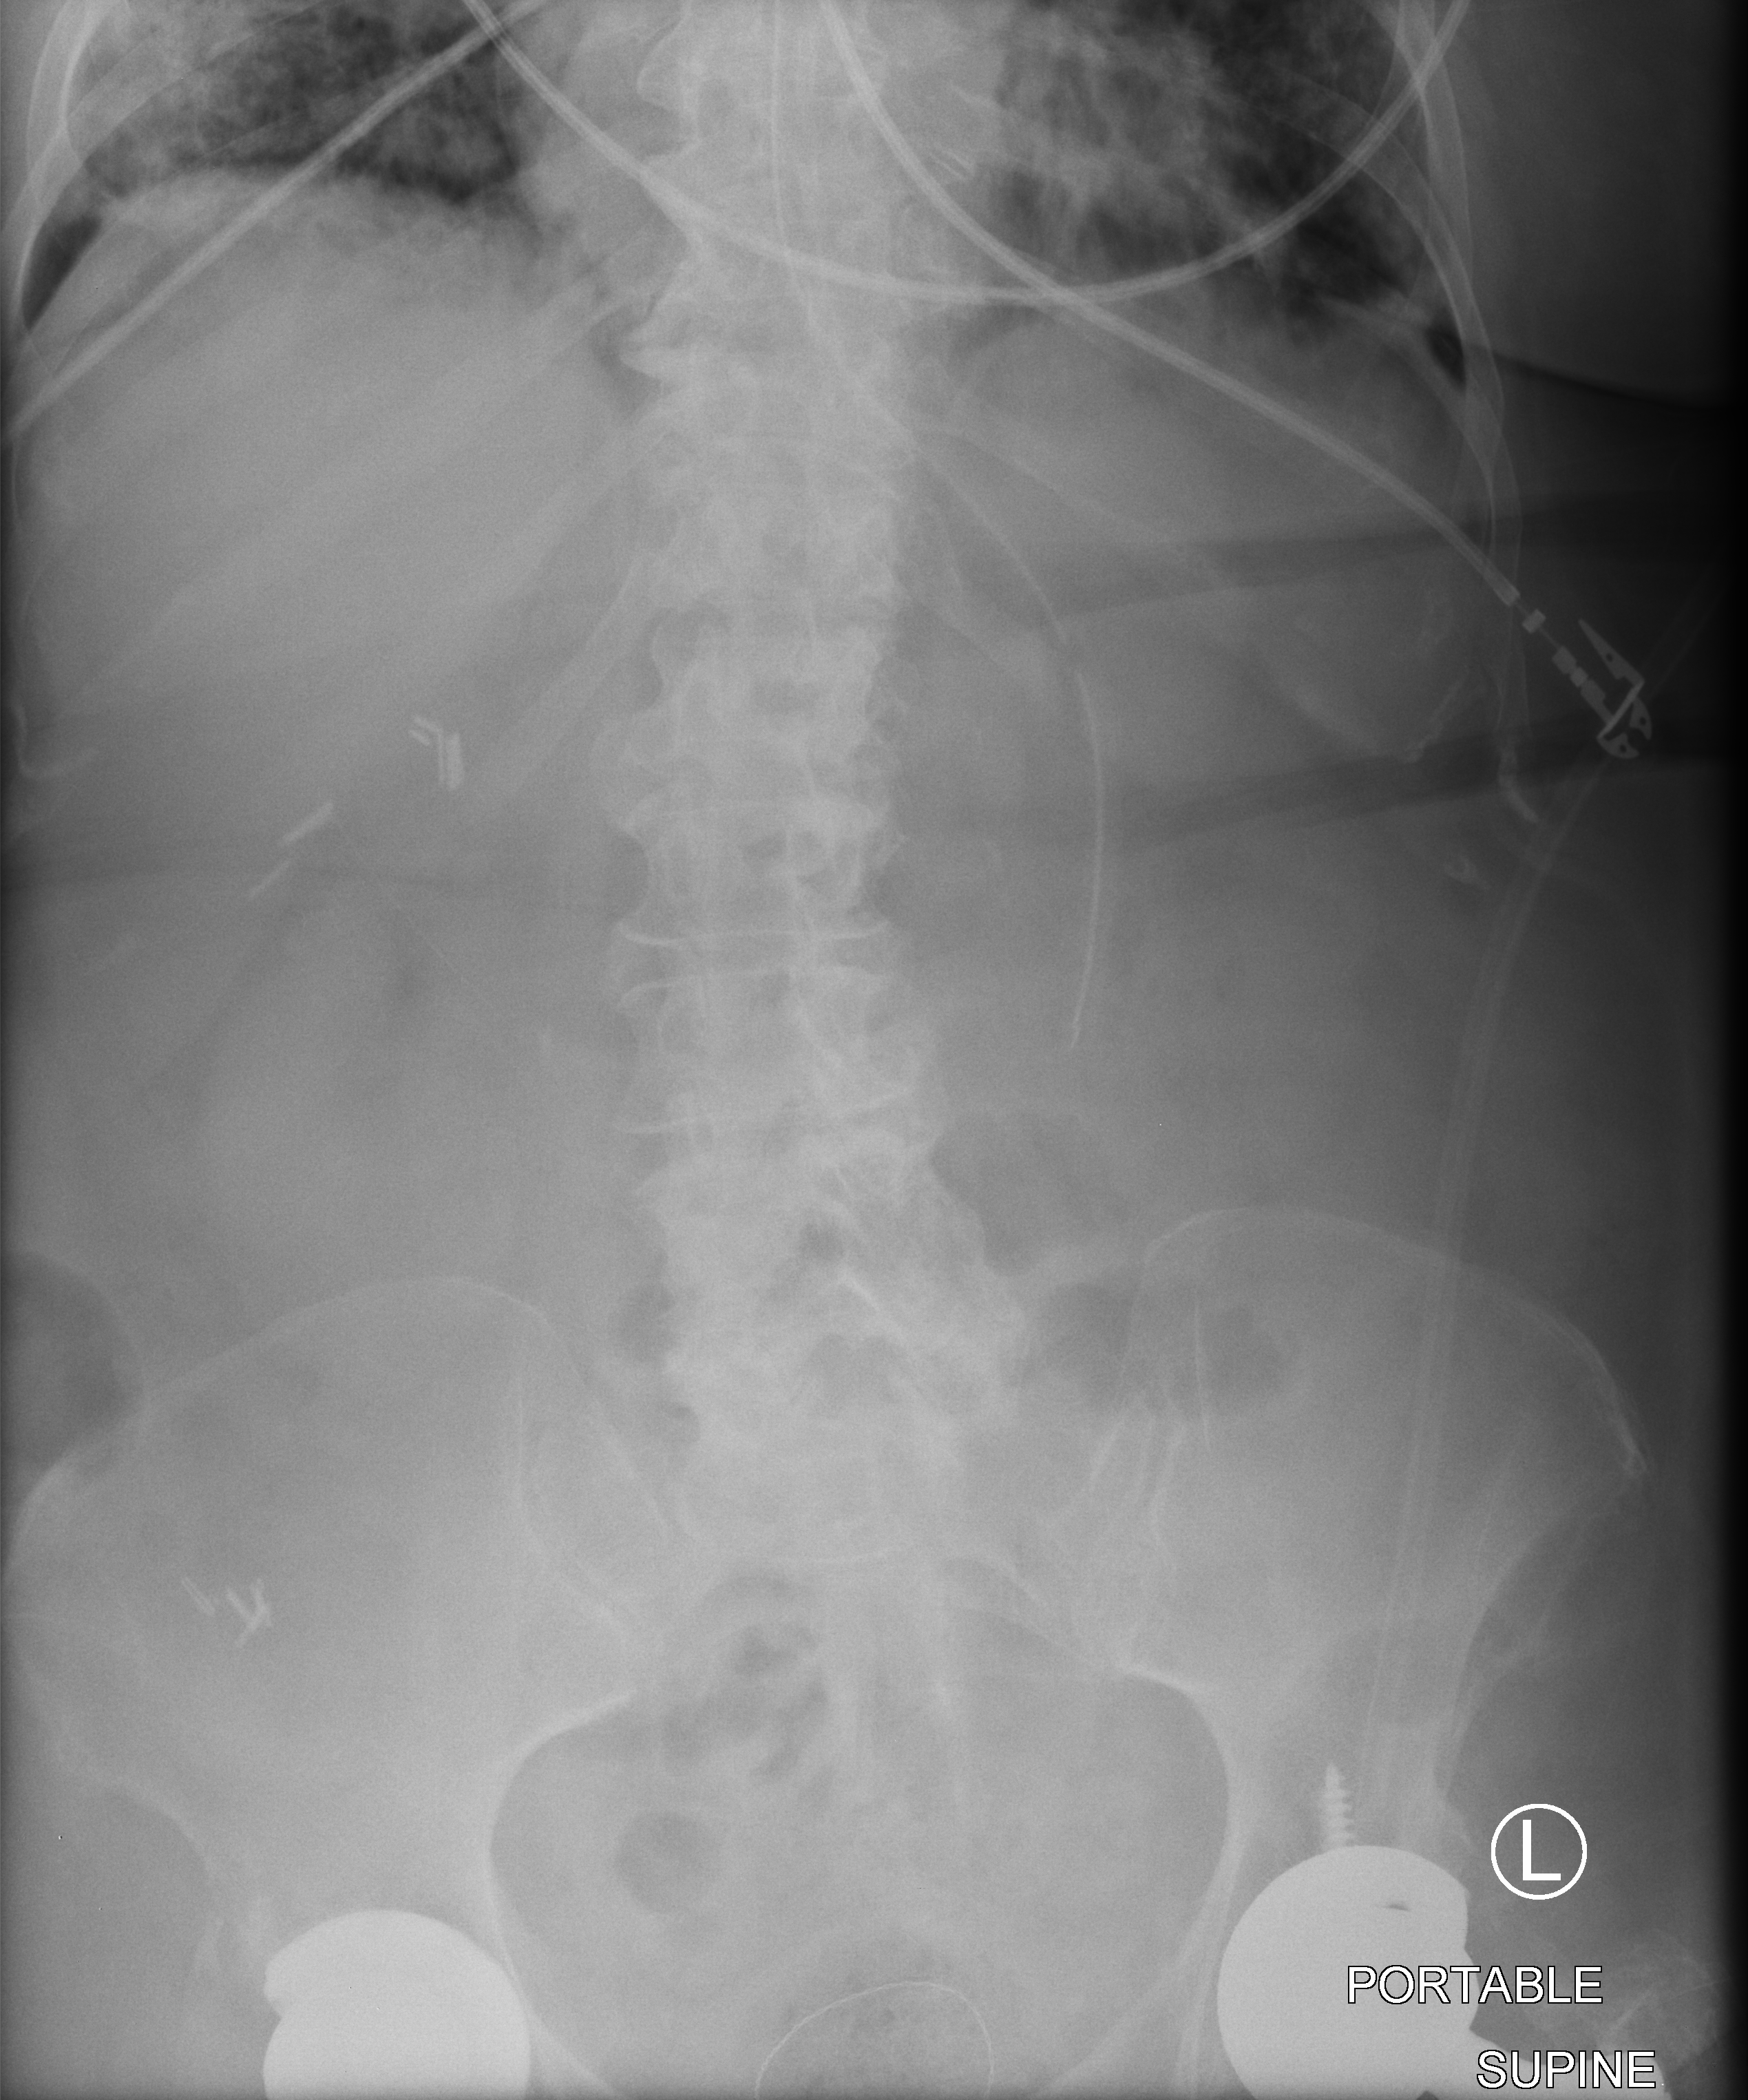
Portable abdomen radiograph, anteroposterior (AP) projection. Patient hospitalised with COVID-19; female, aged 75–90 years.
Hospital-stay facts (about this admission, not read from this image; timing relative to this image not recorded): admitted to intensive care during this hospital stay: no; length of hospital stay: 56 days; mechanically ventilated during this hospital stay: yes.